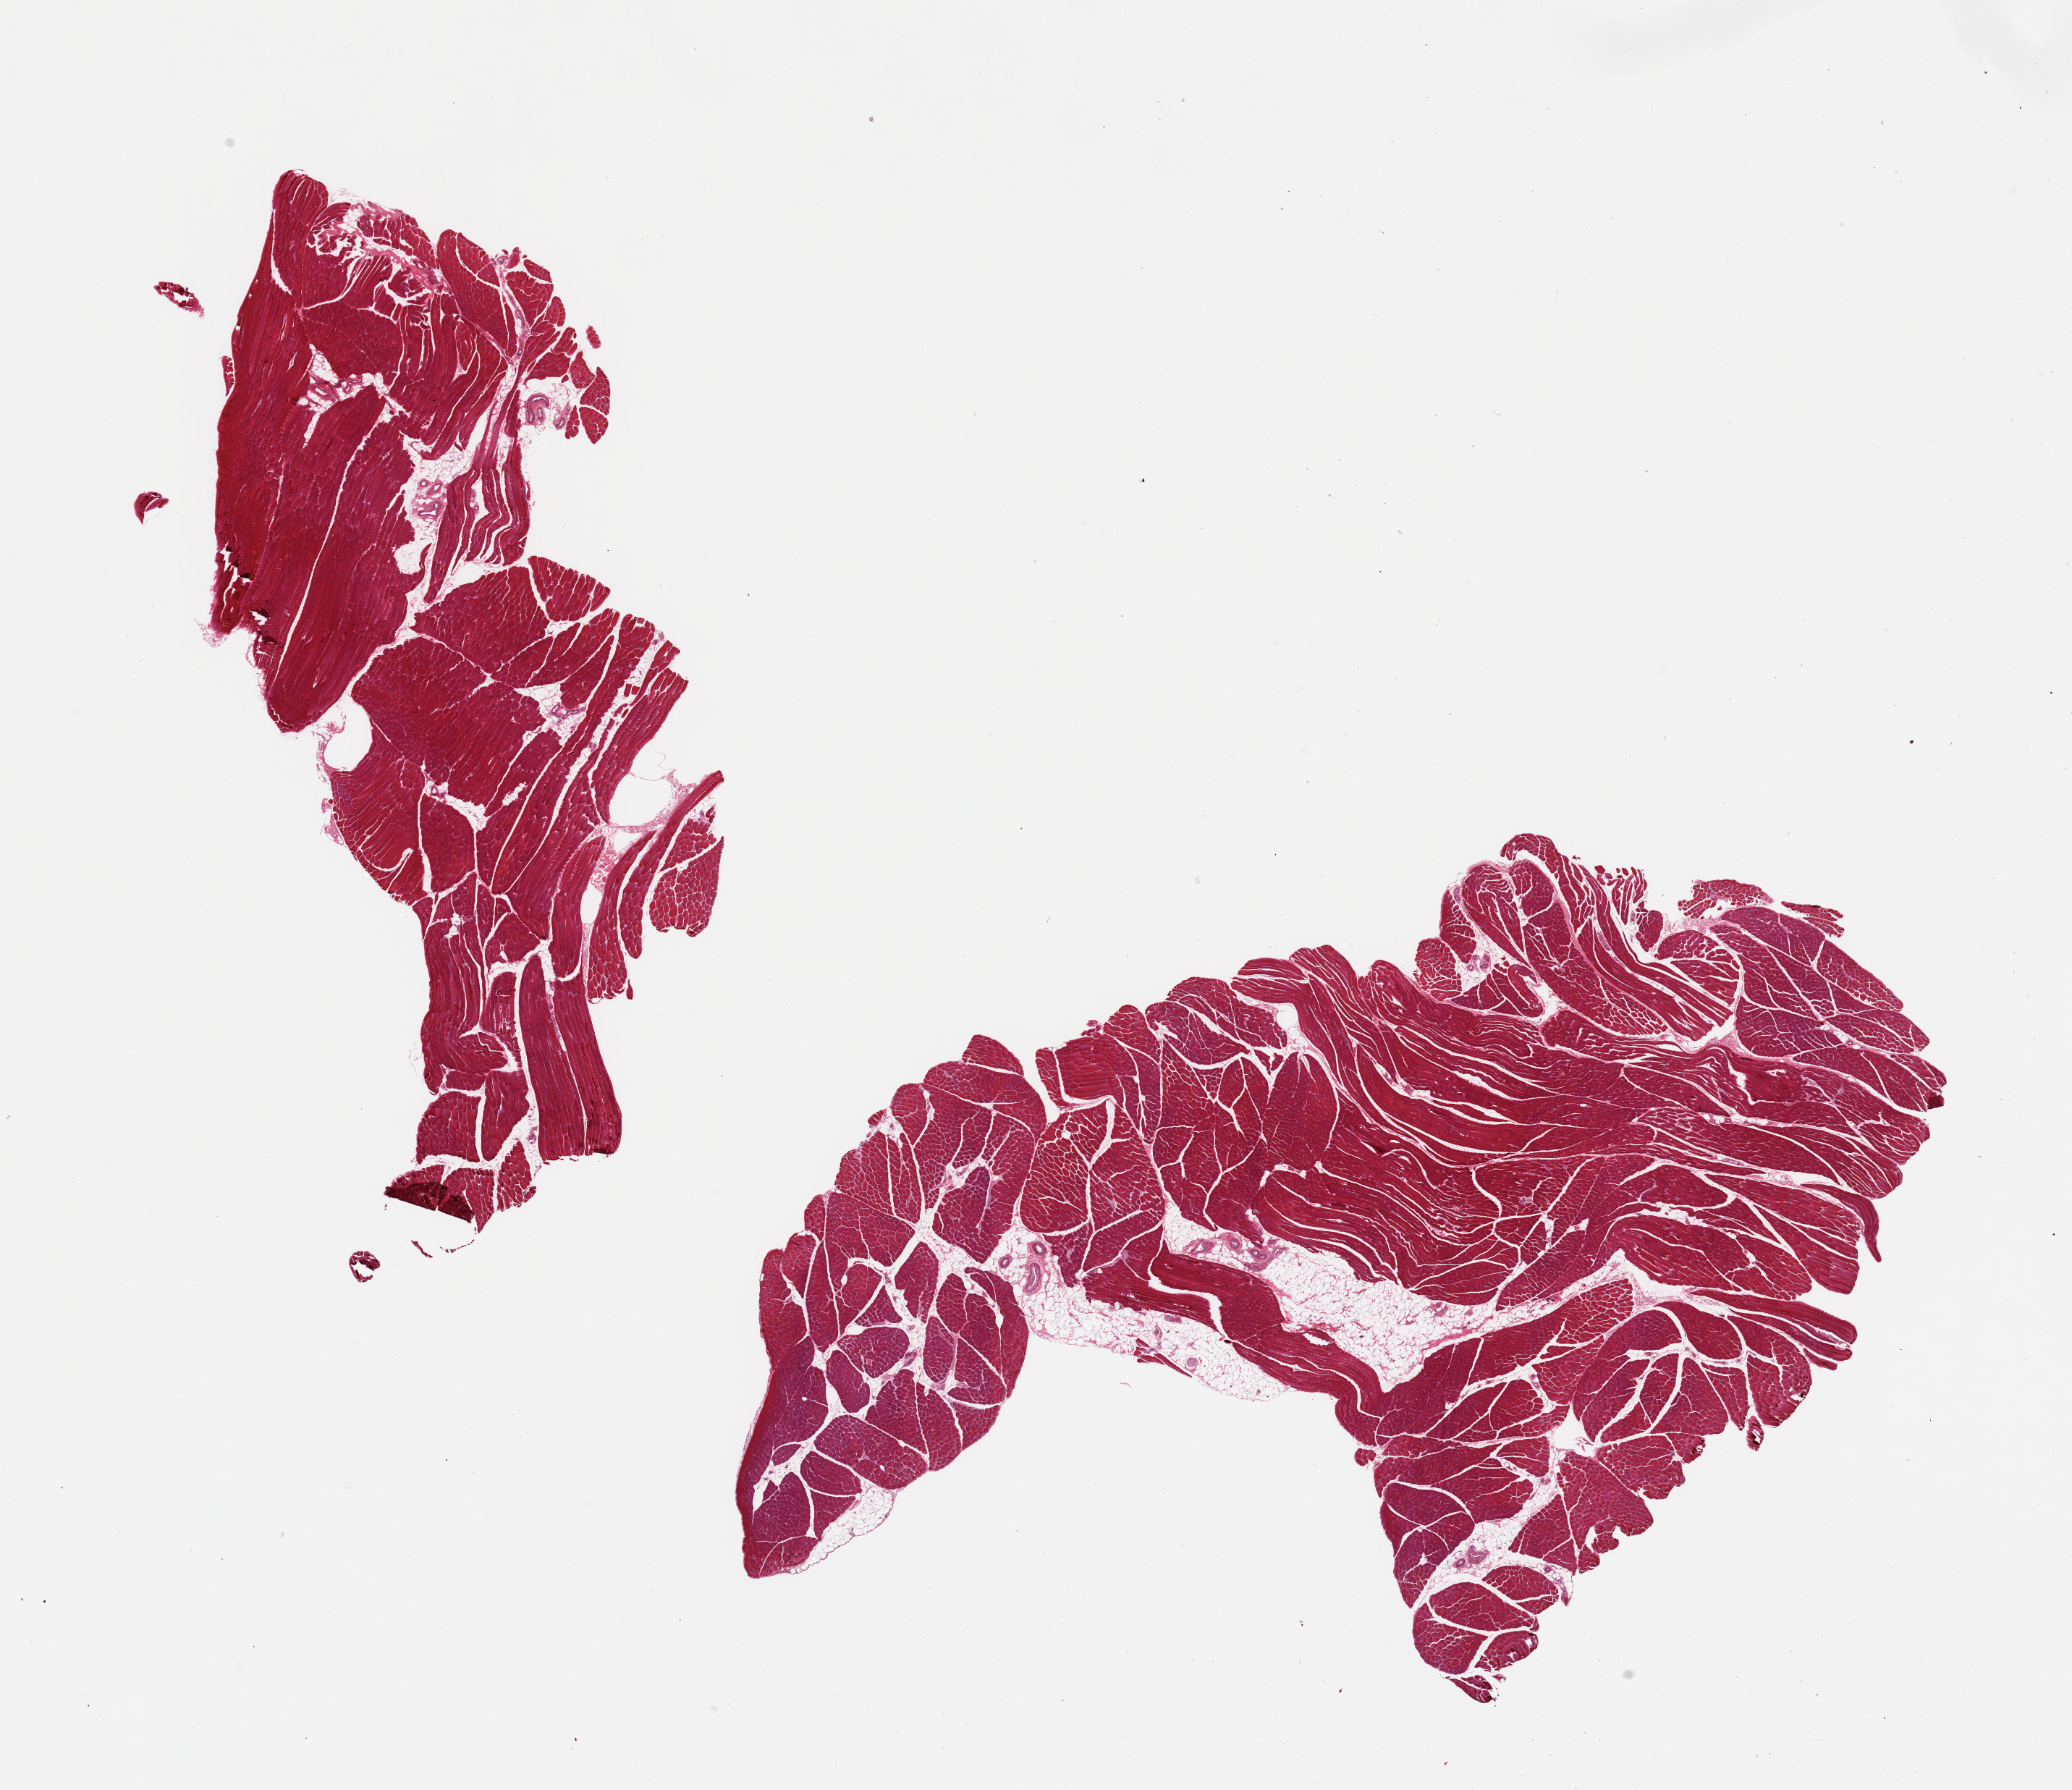
Haematoxylin and eosin whole-slide image — a low-resolution overview of the entire scanned area, about 22.6 x 19.6 mm (slide scanned at 20x). PAXgene-fixed paraffin-embedded (PFPE) section. Section of skeletal muscle (target tissue). Tissue donor sample. Donor: female.
* pathologist's review note for this sample: 2 pieces, 5-10% internal and attached adipose tissue